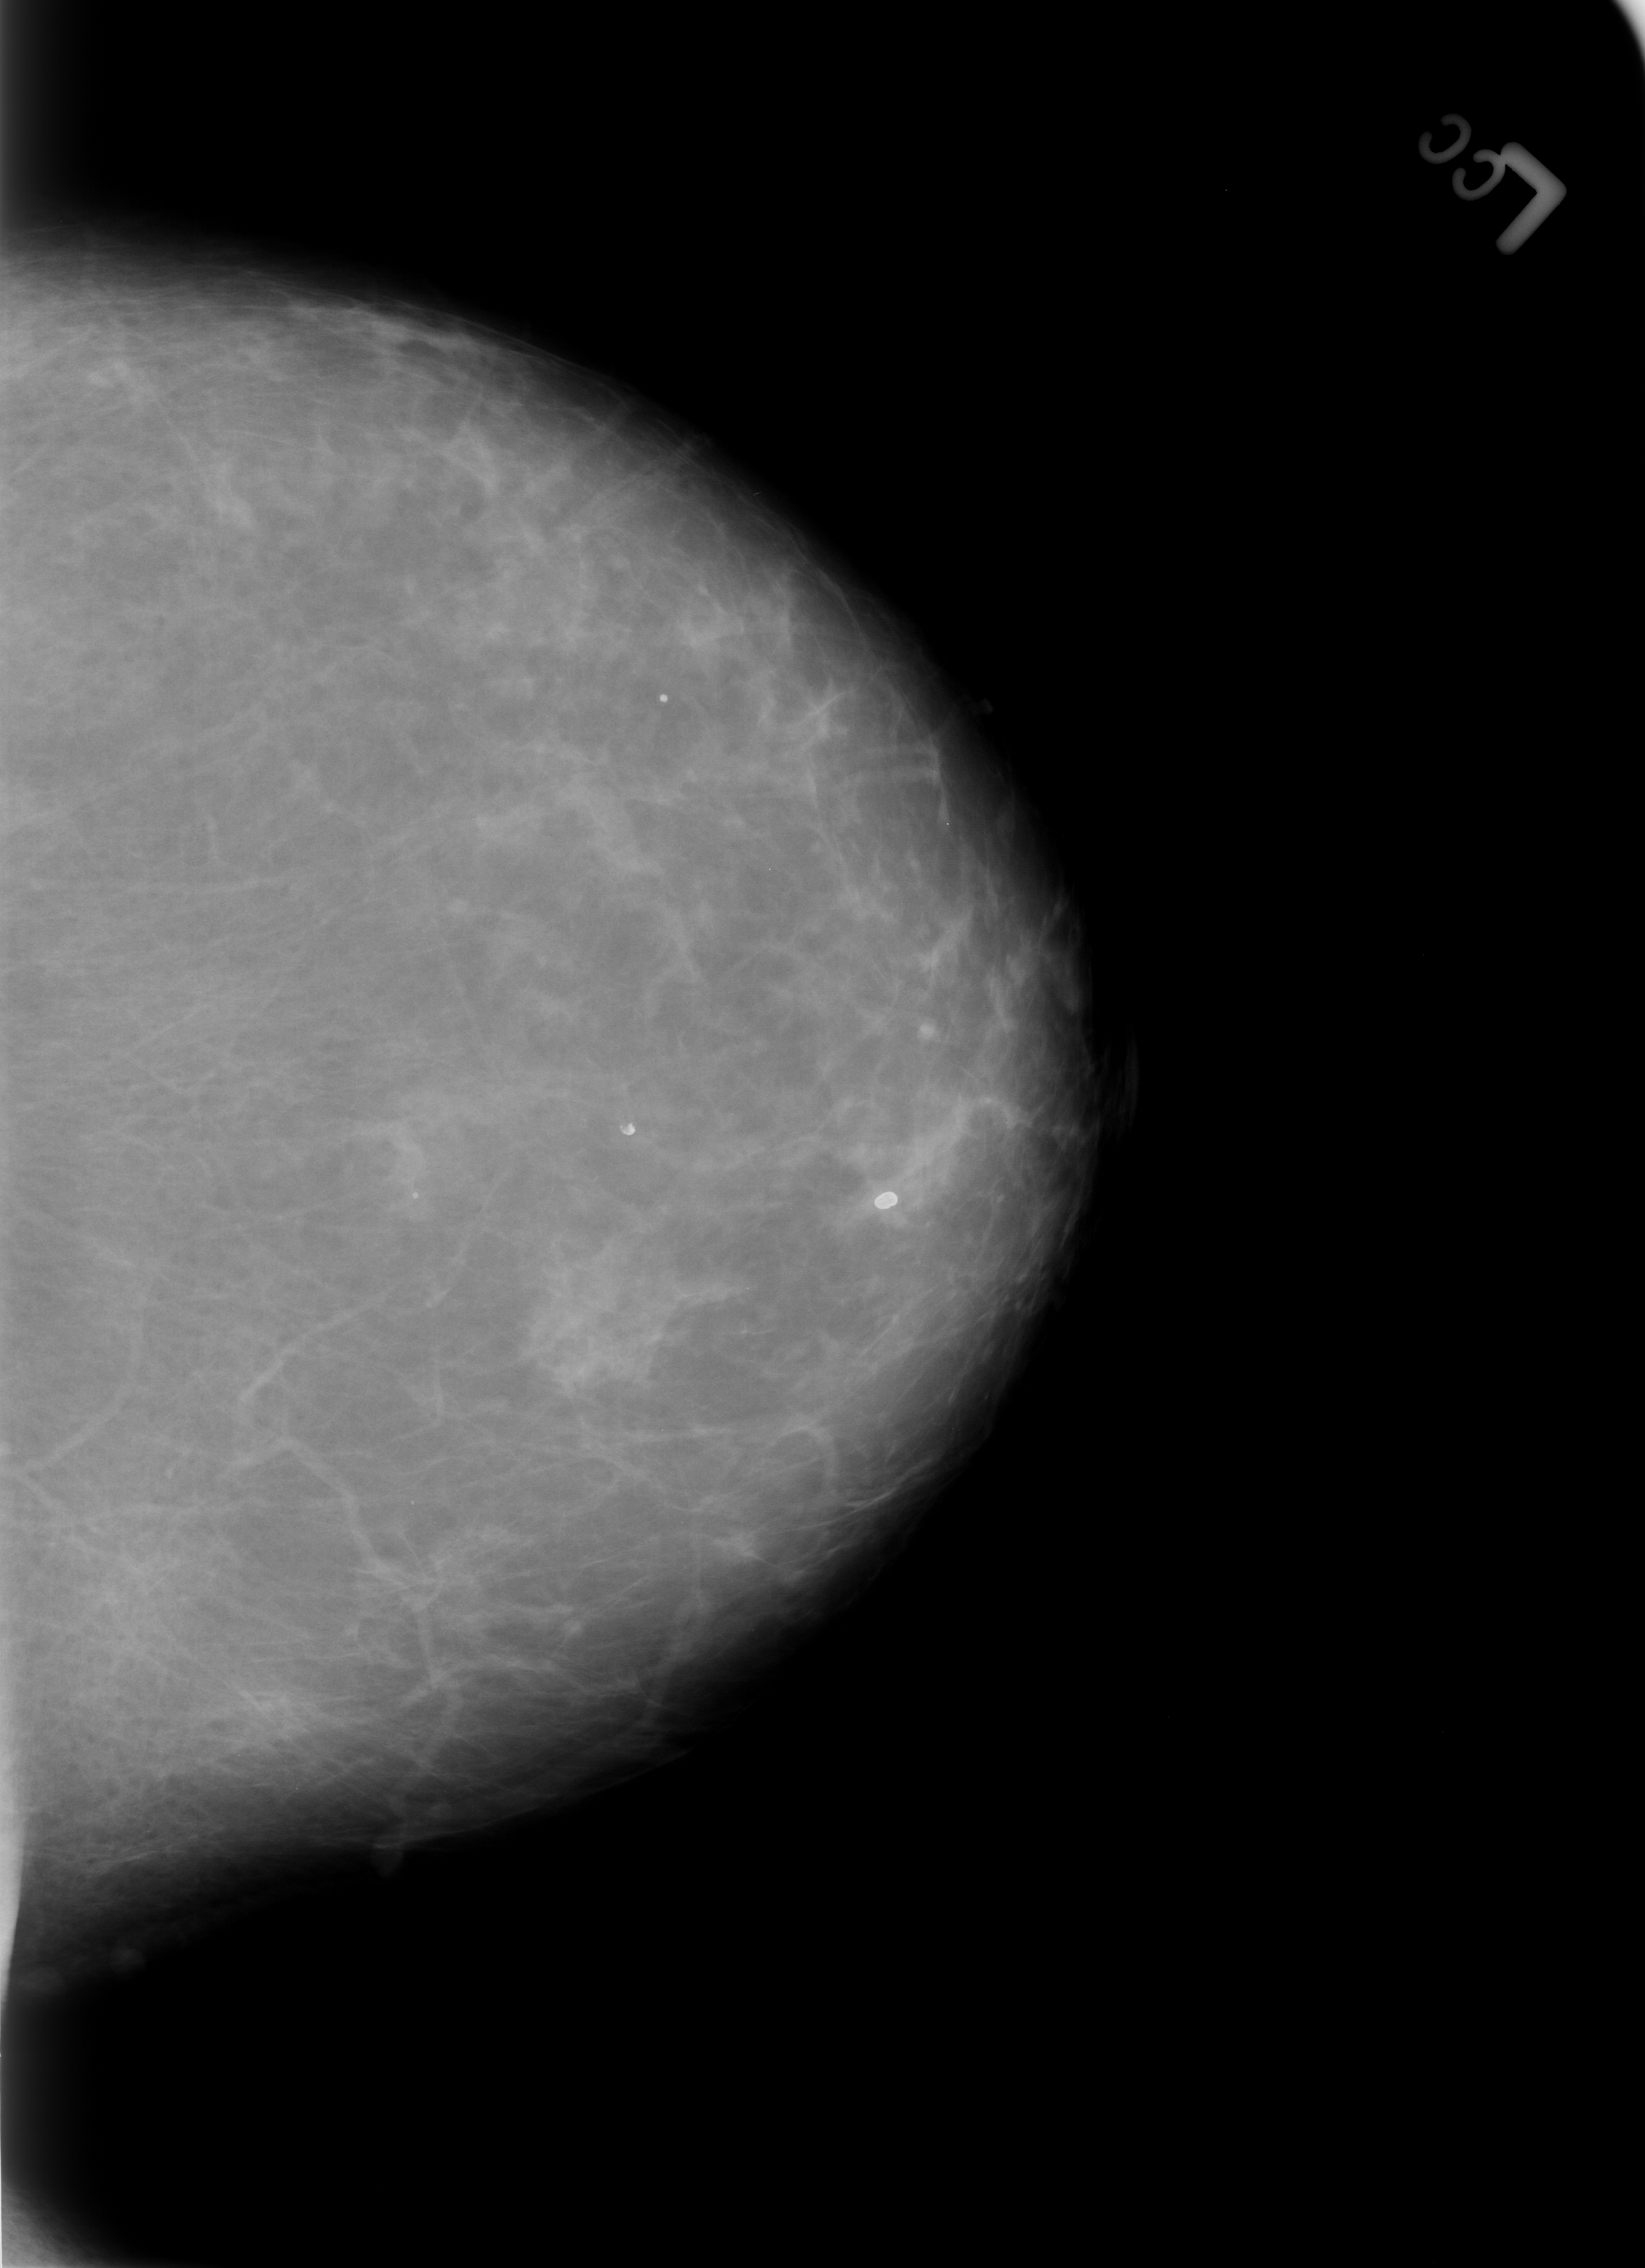
Scanned film-screen mammogram, left breast, CC view, breast composition: scattered fibroglandular densities (BI-RADS density category 2 of 4).
- Marked findings (only marked abnormalities are described; nothing is implied about the rest of the image): Finding 1 of 3: calcifications, morphology lucent center; BI-RADS assessment category 2; benign without callback (not worked up further).
- Finding 2 of 3: calcifications, morphology lucent center; BI-RADS assessment category 2; subtlety rating 5 on a 1 (subtle) to 5 (obvious) scale; benign; no additional work-up was recommended (benign without callback).
- Finding 3 of 3: calcifications, morphology lucent center; BI-RADS assessment category 2; subtlety rating 5 on a 1 (subtle) to 5 (obvious) scale; benign without callback (not worked up further).